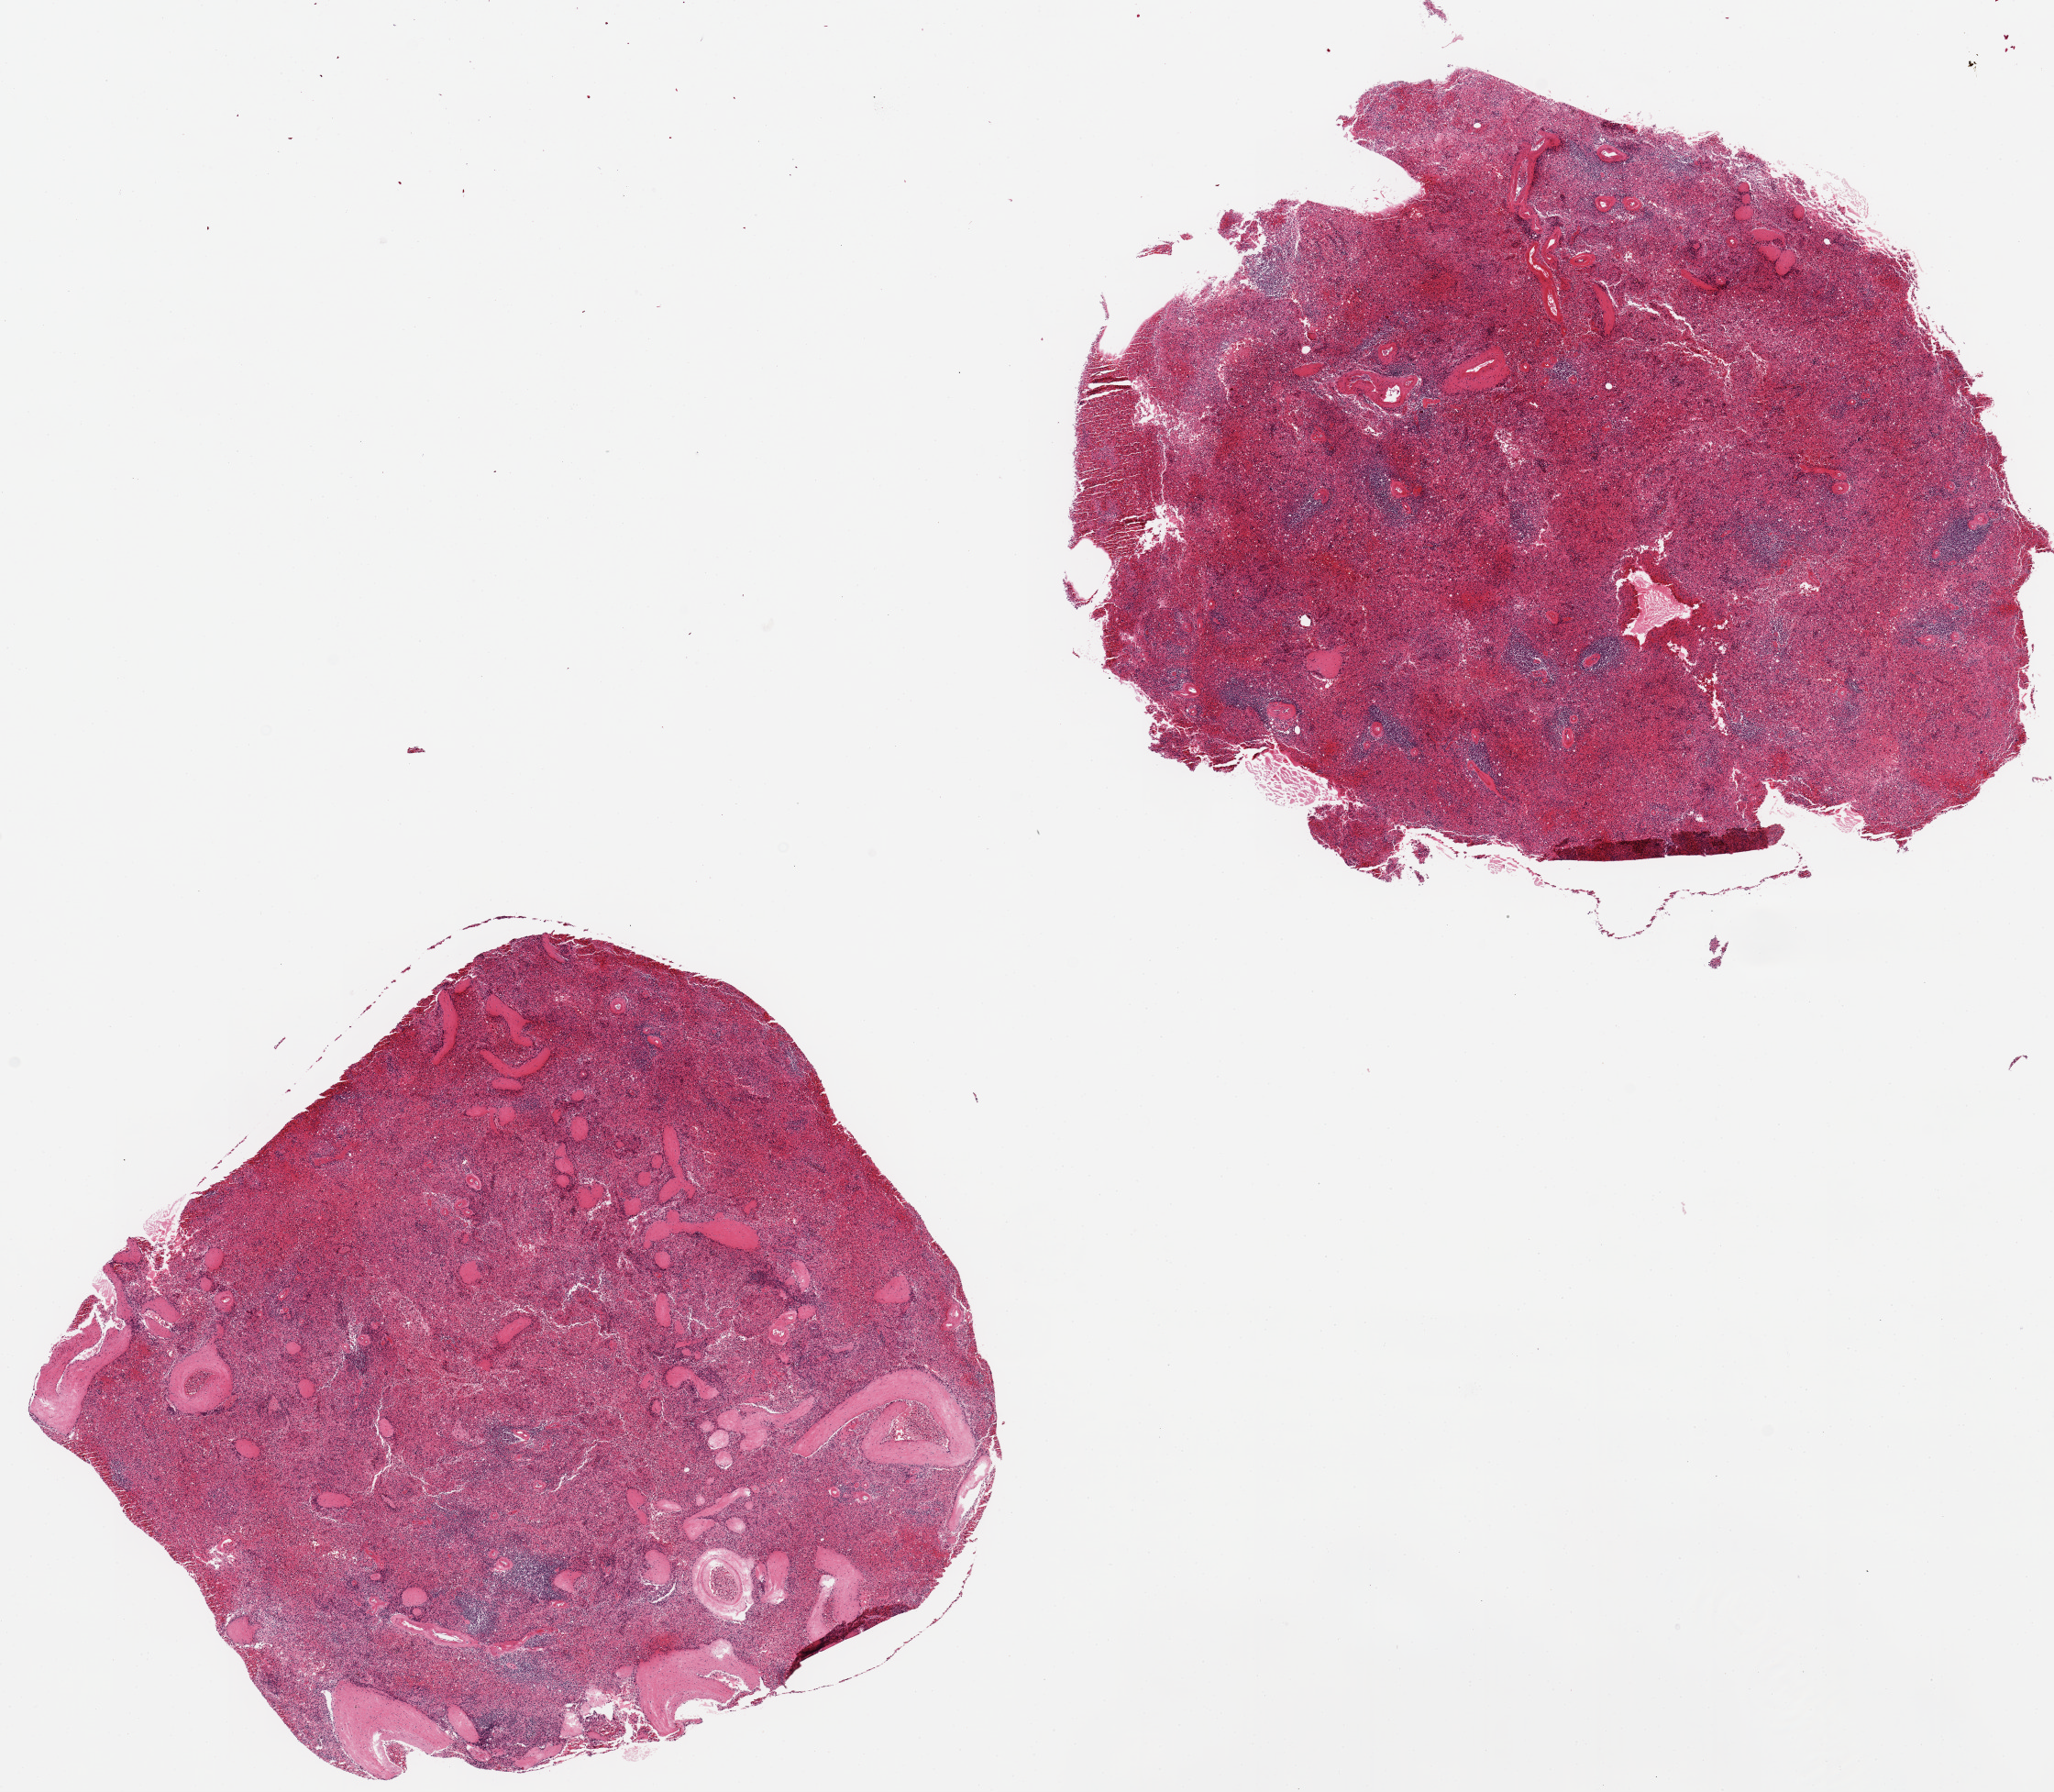
Digitized haematoxylin and eosin-stained section — low-resolution overview of the scanned area, about 17.7 x 15.5 mm (from a 20x scan), PAXgene-fixed paraffin-embedded (PFPE) section, sampled site (target tissue): spleen, tissue donor sample.
Review note (as recorded): 2 pieces, 7x7 & 8x7mm; congested.